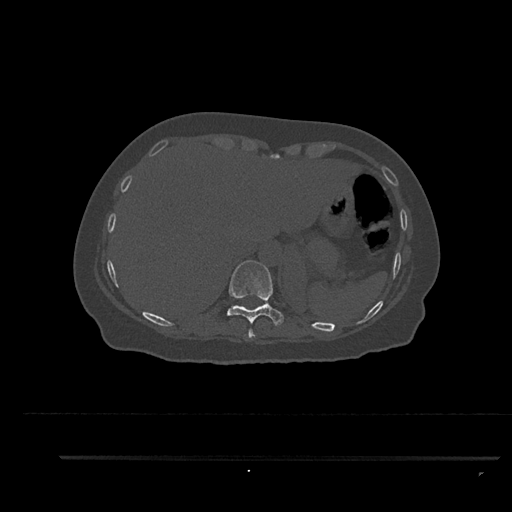
CT including the spine, one axial slice; position 364 of 797 along the scan axis; bone window (W 1800 / L 400 HU); 512 × 512 image matrix, field of view 408 × 408 mm. Female patient, age 44 years. From the clinical record (not read from this slice): primary cancer: renal.
Annotated regions visible in this slice (semi-automatically segmented with operator editing):
- T10 vertebra: bounding box <227,260,284,331> (left, top, right, bottom; pixels)
- T9 vertebra: <244,329,256,338>